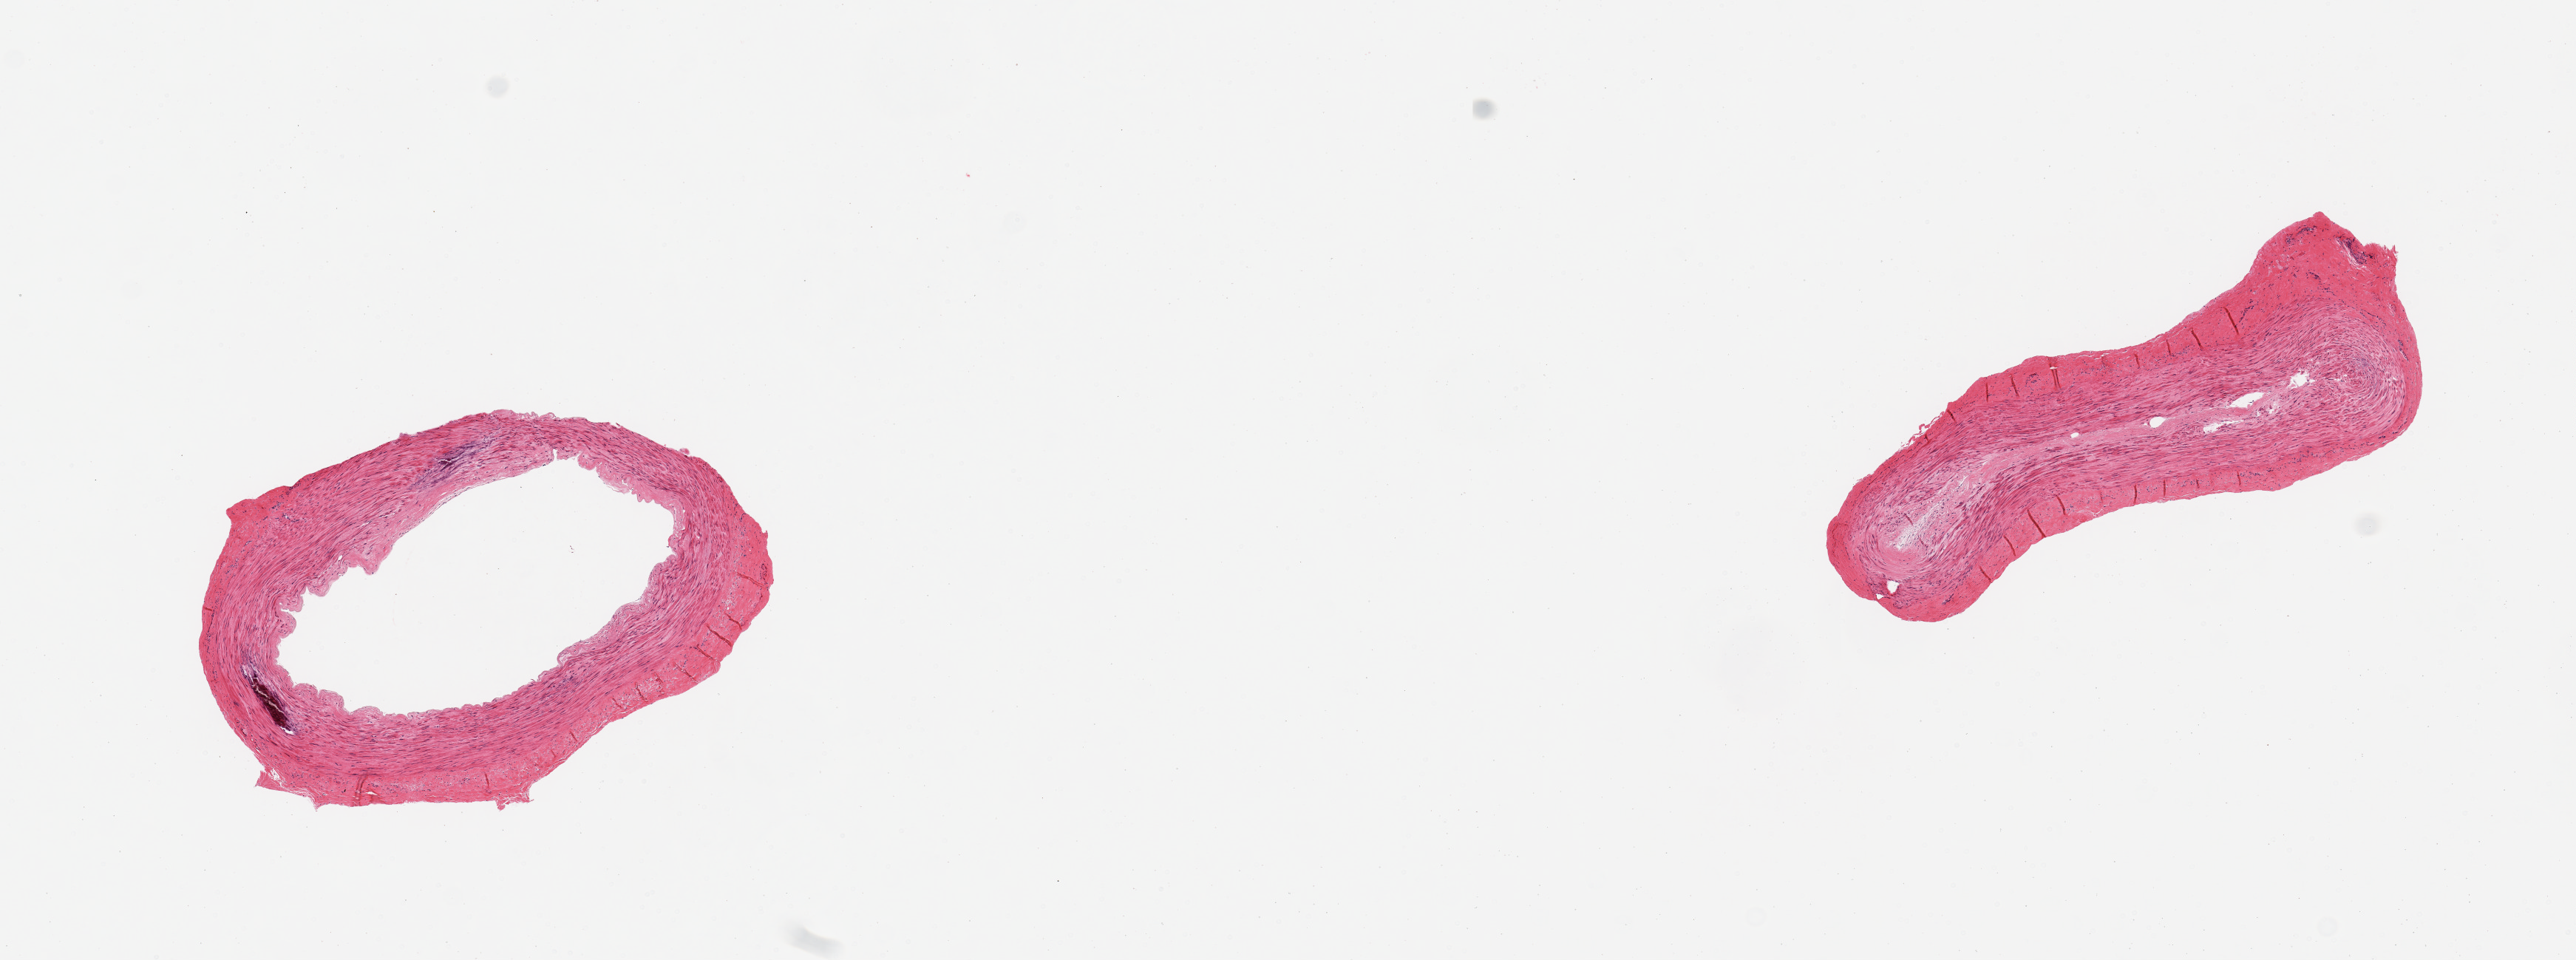
Whole-slide image, H&E stain, whole scanned area (about 13.8 x 5.1 mm, acquisition: 20x scan) shown as a low-resolution overview, PAXgene-fixed, paraffin-embedded tissue, section of tibial artery (target tissue), tissue donor sample. Donor: male.
Reviewer comment on this tissue sample: 2 pieces; fibrosclerotic plaque and medial calcifications.